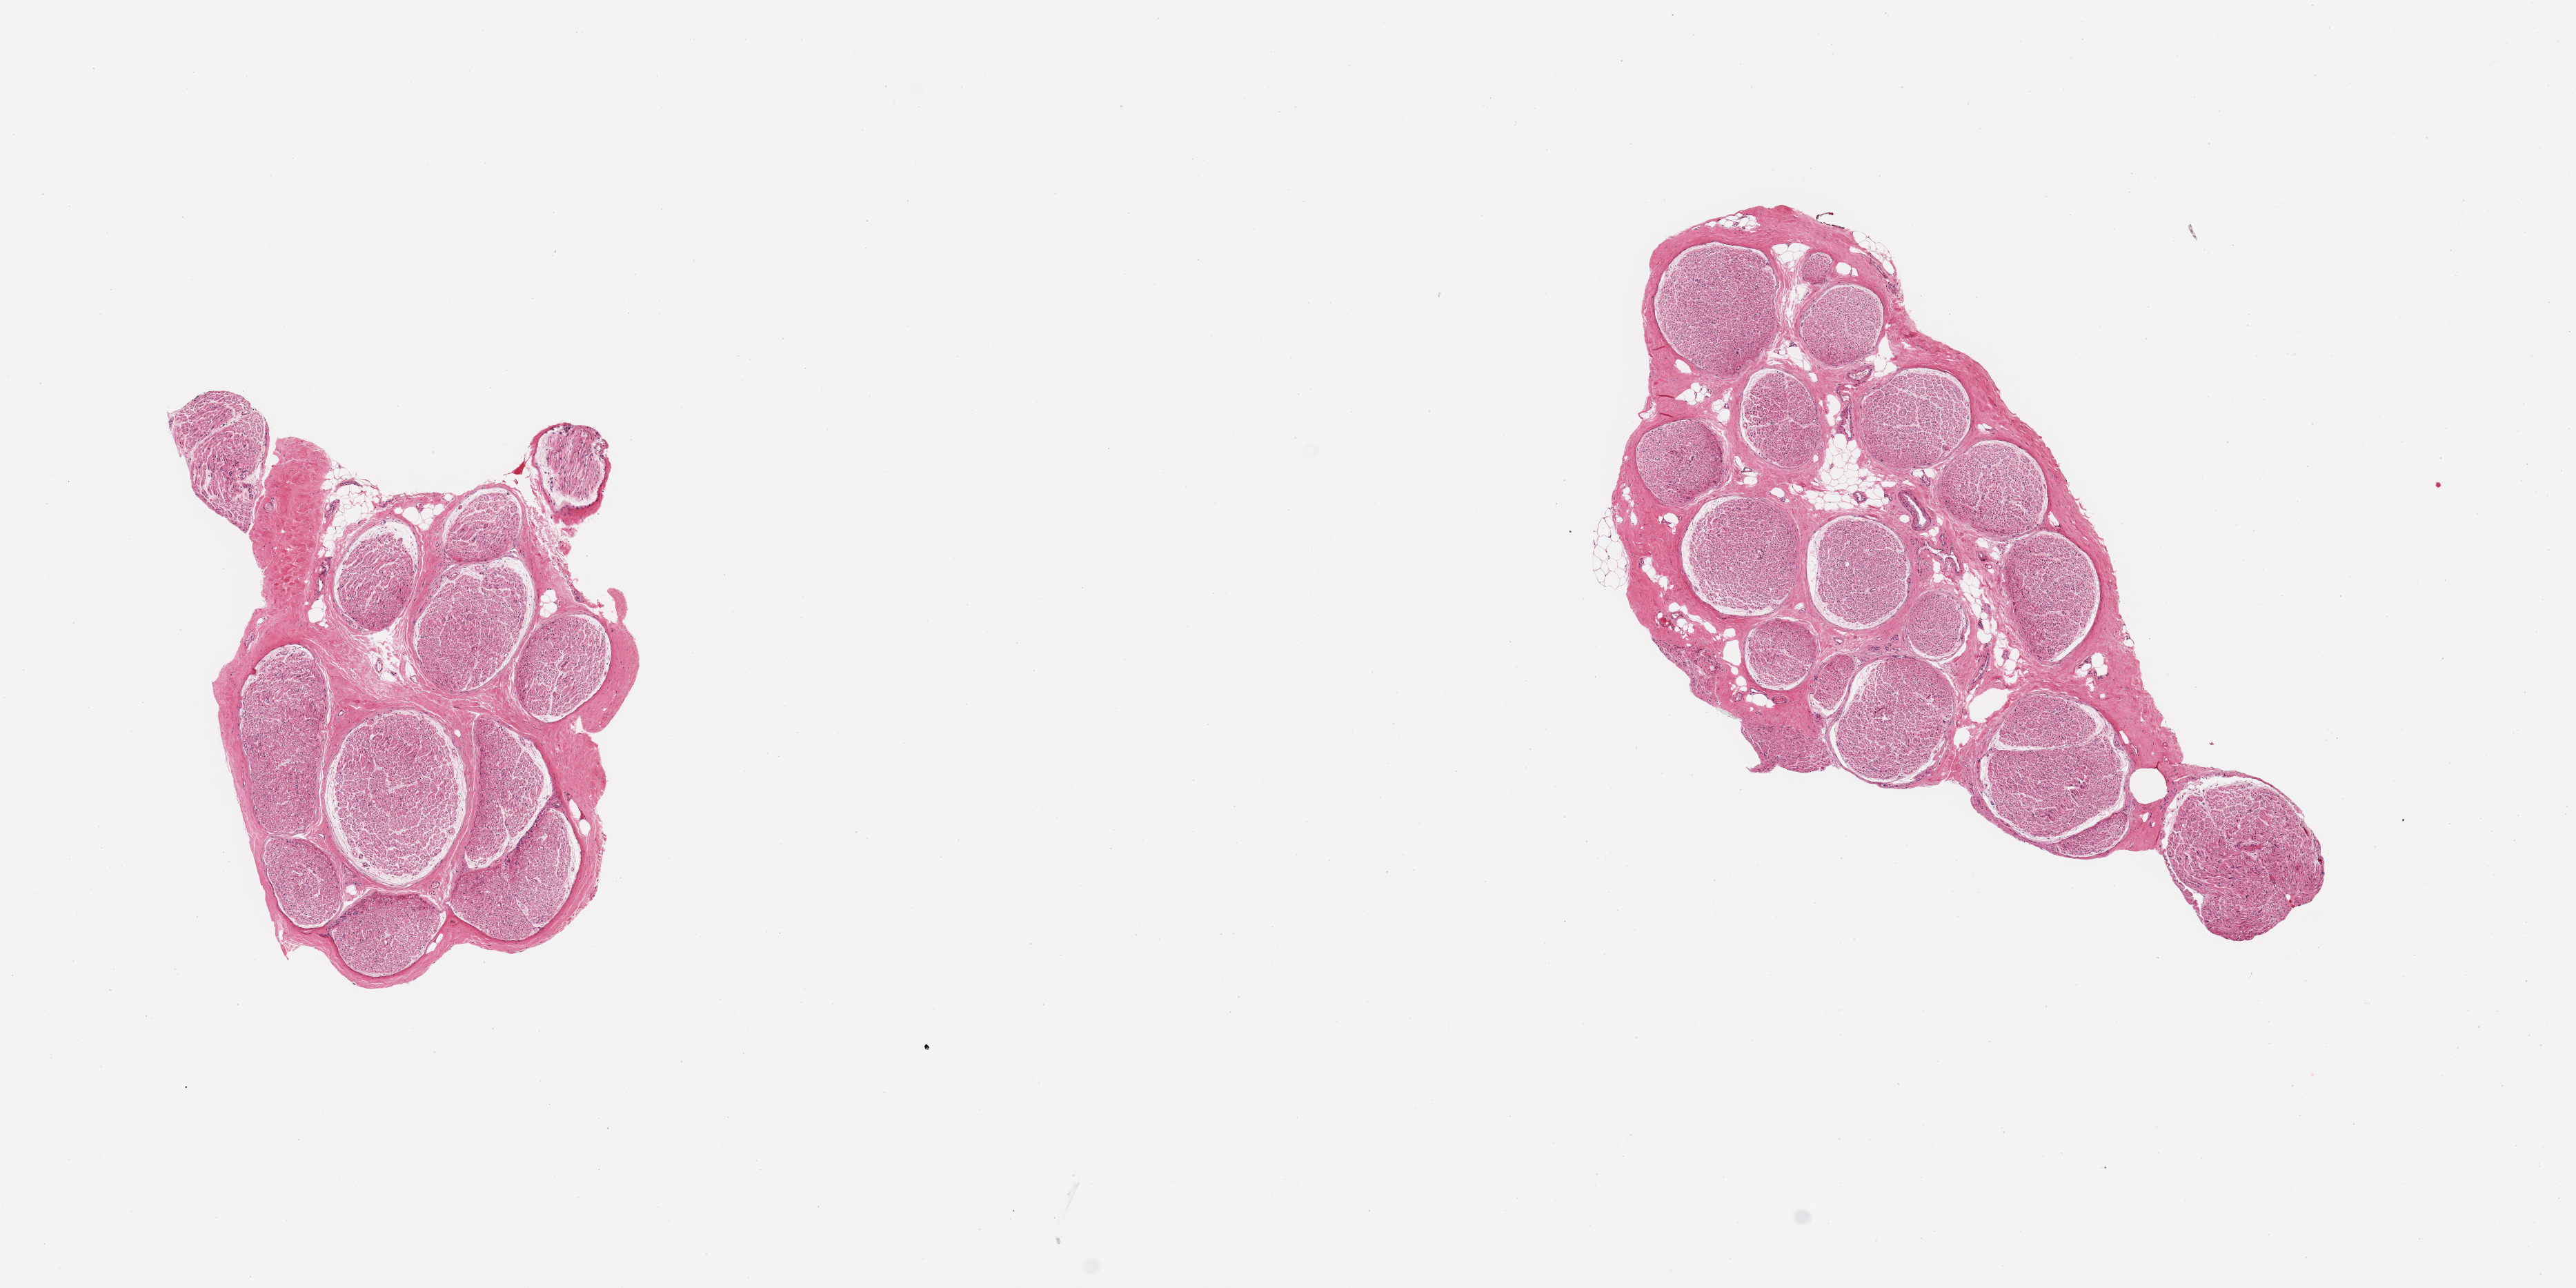
Whole-slide image, haematoxylin and eosin stain — low-resolution overview of the scanned area, about 14.8 x 7.4 mm, PAXgene-fixed paraffin-embedded (PFPE) section, target tissue: tibial nerve, donor tissue sample. Donor: female.
- pathologist's review note for this sample: 2 pieces; 5% internal fat; well trimmed